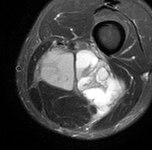
MRI of an extremity soft-tissue mass, one axial slice; position 31 of 90 along the scan axis; STIR; MR volume resampled by the dataset authors to the PET/CT grid (not the native acquisition matrix); 152 × 150 image matrix, field of view 148 × 146 mm. Male patient. Case-level facts recorded for this patient, not image findings: histological type: undifferentiated pleomorphic liposarcoma; grade: high; site of the primary tumour: left thigh.
Structures marked on this image (expert contour drawn on MRI and transferred to this co-registered scan by the dataset authors):
- gross tumour volume including surrounding oedema: bounding box [x1, y1, x2, y2] px = [34, 41, 122, 122]
- gross tumour volume (mass): [45, 57, 110, 104]